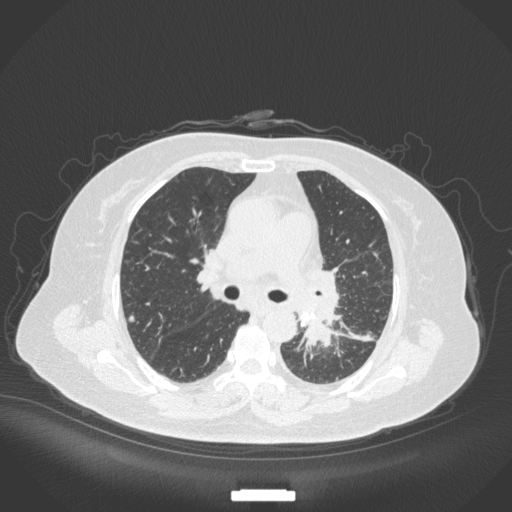
Chest CT, one axial slice; position 210 of 328 along the scan axis; reconstruction kernel B31f; 120 kVp; lung window (W 1500 / L -600 HU); 512 × 512 image matrix, field of view 400 × 400 mm. Female patient, age 69 years. Case-level facts recorded for this patient, not image findings: clinical TNM (as recorded): T2b N3 M1.
Structures marked on this image (rectangle marked by the reading radiologist):
- lung tumour (recorded histology: adenocarcinoma): bounding box [x1, y1, x2, y2] px = [294, 311, 337, 353]